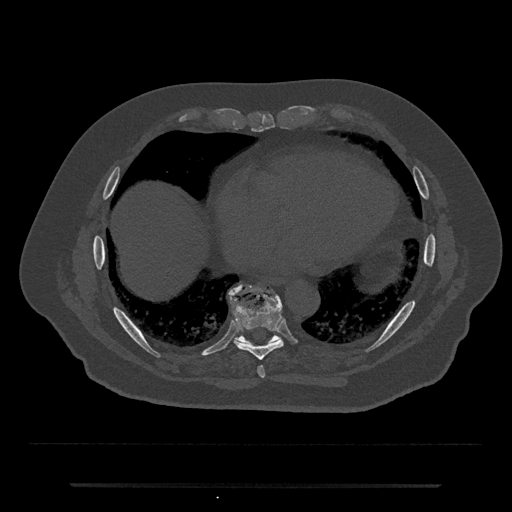
CT including the spine, one axial slice. Slice 795 of 797 in the series (ordered by position). 120 kVp. Bone window (W 1800 / L 400 HU). 0.5 mm slice thickness. 512 × 512 image matrix, field of view 434 × 434 mm. Male patient, age 80 years. From the clinical record (not read from this slice): primary cancer: prostate.
Structures marked on this image (semi-automatically segmented with operator editing):
- T8 vertebra: box from (x=233, y=298) to (x=283, y=361) px
- T9 vertebra: (x=229, y=284)–(x=281, y=347)